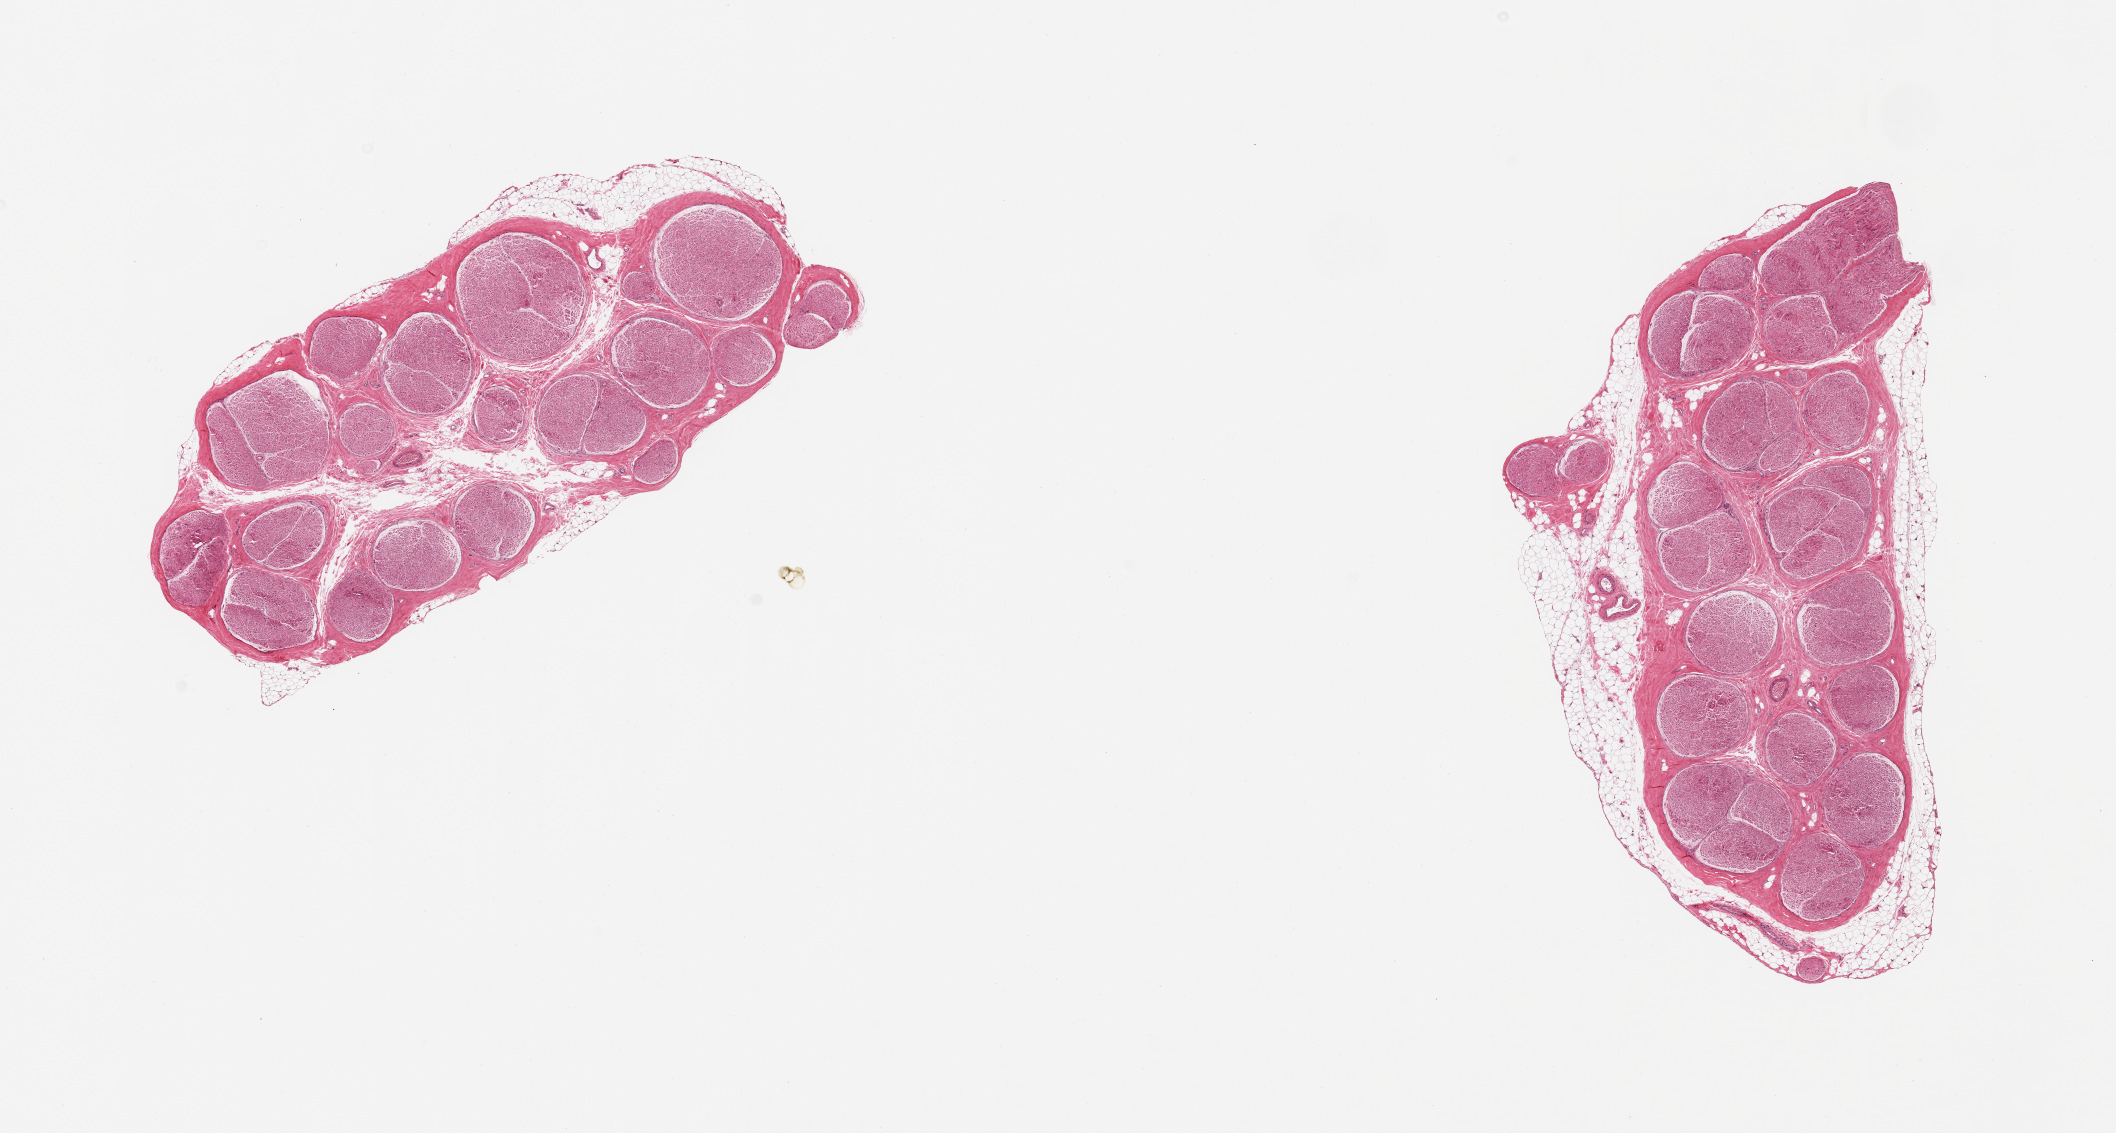
Digitized haematoxylin and eosin-stained section, brightfield, low-resolution overview of the scanned area, about 16.7 x 9.0 mm (acquisition: 20x scan), PAXgene-fixed, paraffin-embedded tissue, sampled site (target tissue): tibial nerve, donor tissue sample. Donor sex: female.
Reviewer comment on this tissue sample: 2 pieces; 10 & 20% external fat & fibrous content.